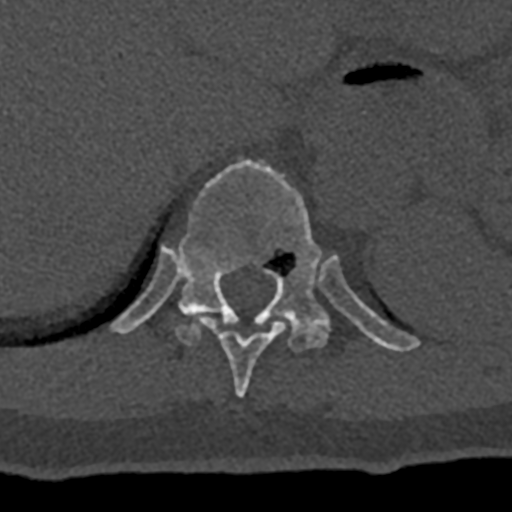
CT including the spine, one axial slice; position 569 of 797 along the scan axis; bone window (W 1800 / L 400 HU); 512 × 512 image matrix. Patient: male, 74 years. Case-level facts recorded for this patient, not image findings: primary cancer: renal; vertebrae with lytic lesions (as recorded): T10, L1, L2, L3, L4, L5.
Outlined on this slice (semi-automatically segmented with operator editing):
- T10 vertebra: bounding box [x1, y1, x2, y2] px = [197, 316, 287, 397]
- T11 vertebra: [110, 159, 420, 352]